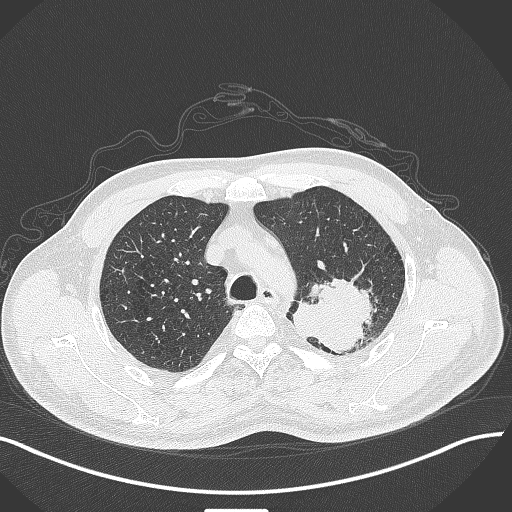
Chest CT, one axial slice; position 328 of 429 along the scan axis; reconstruction kernel B70f; 120 kVp; lung window (W 1500 / L -600 HU); 1 mm slice thickness; 512 × 512 image matrix. Patient: male, 55 years. Case-level facts recorded for this patient, not image findings: clinical TNM (as recorded): T3 N0 M1c.
Outlined on this slice (bounding box drawn by a radiologist):
- lung tumour (recorded histology: adenocarcinoma): box from (x=293, y=272) to (x=375, y=354) px